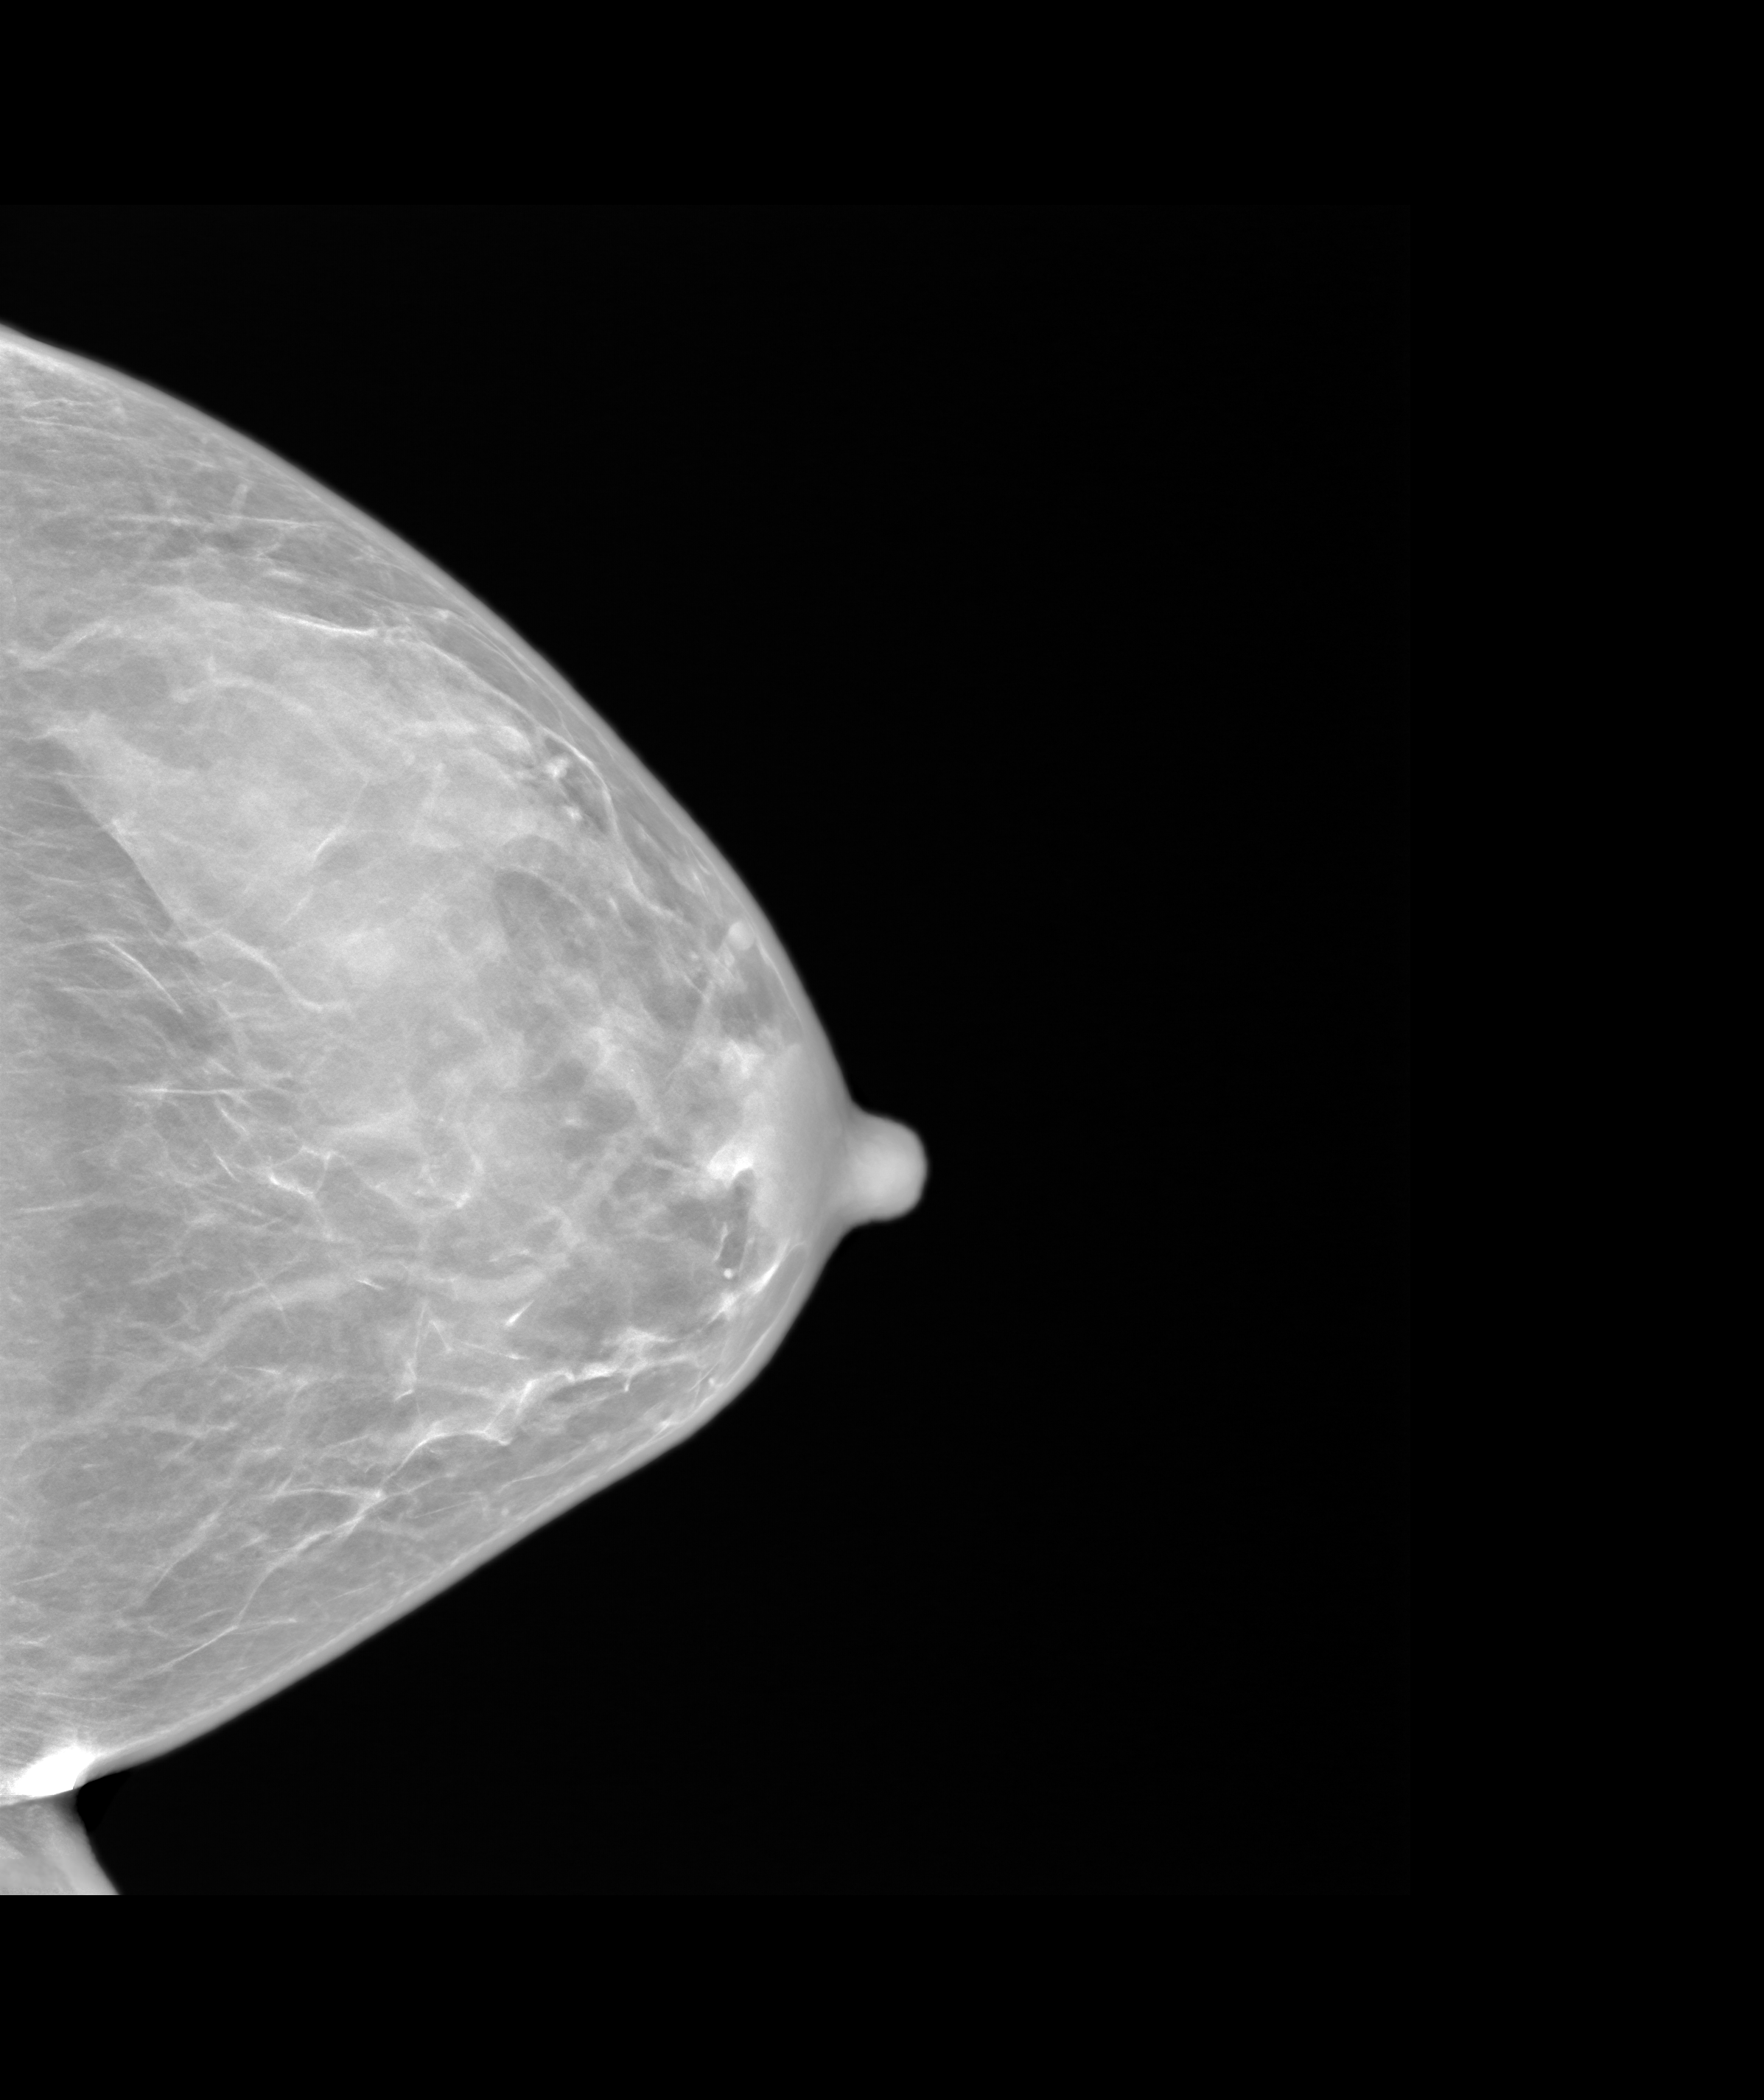
Screening examination. Patient: female, 56 years.
Image type: synthesized 2-D view from tomosynthesis. Breast: left. Projection: craniocaudal (CC) view.